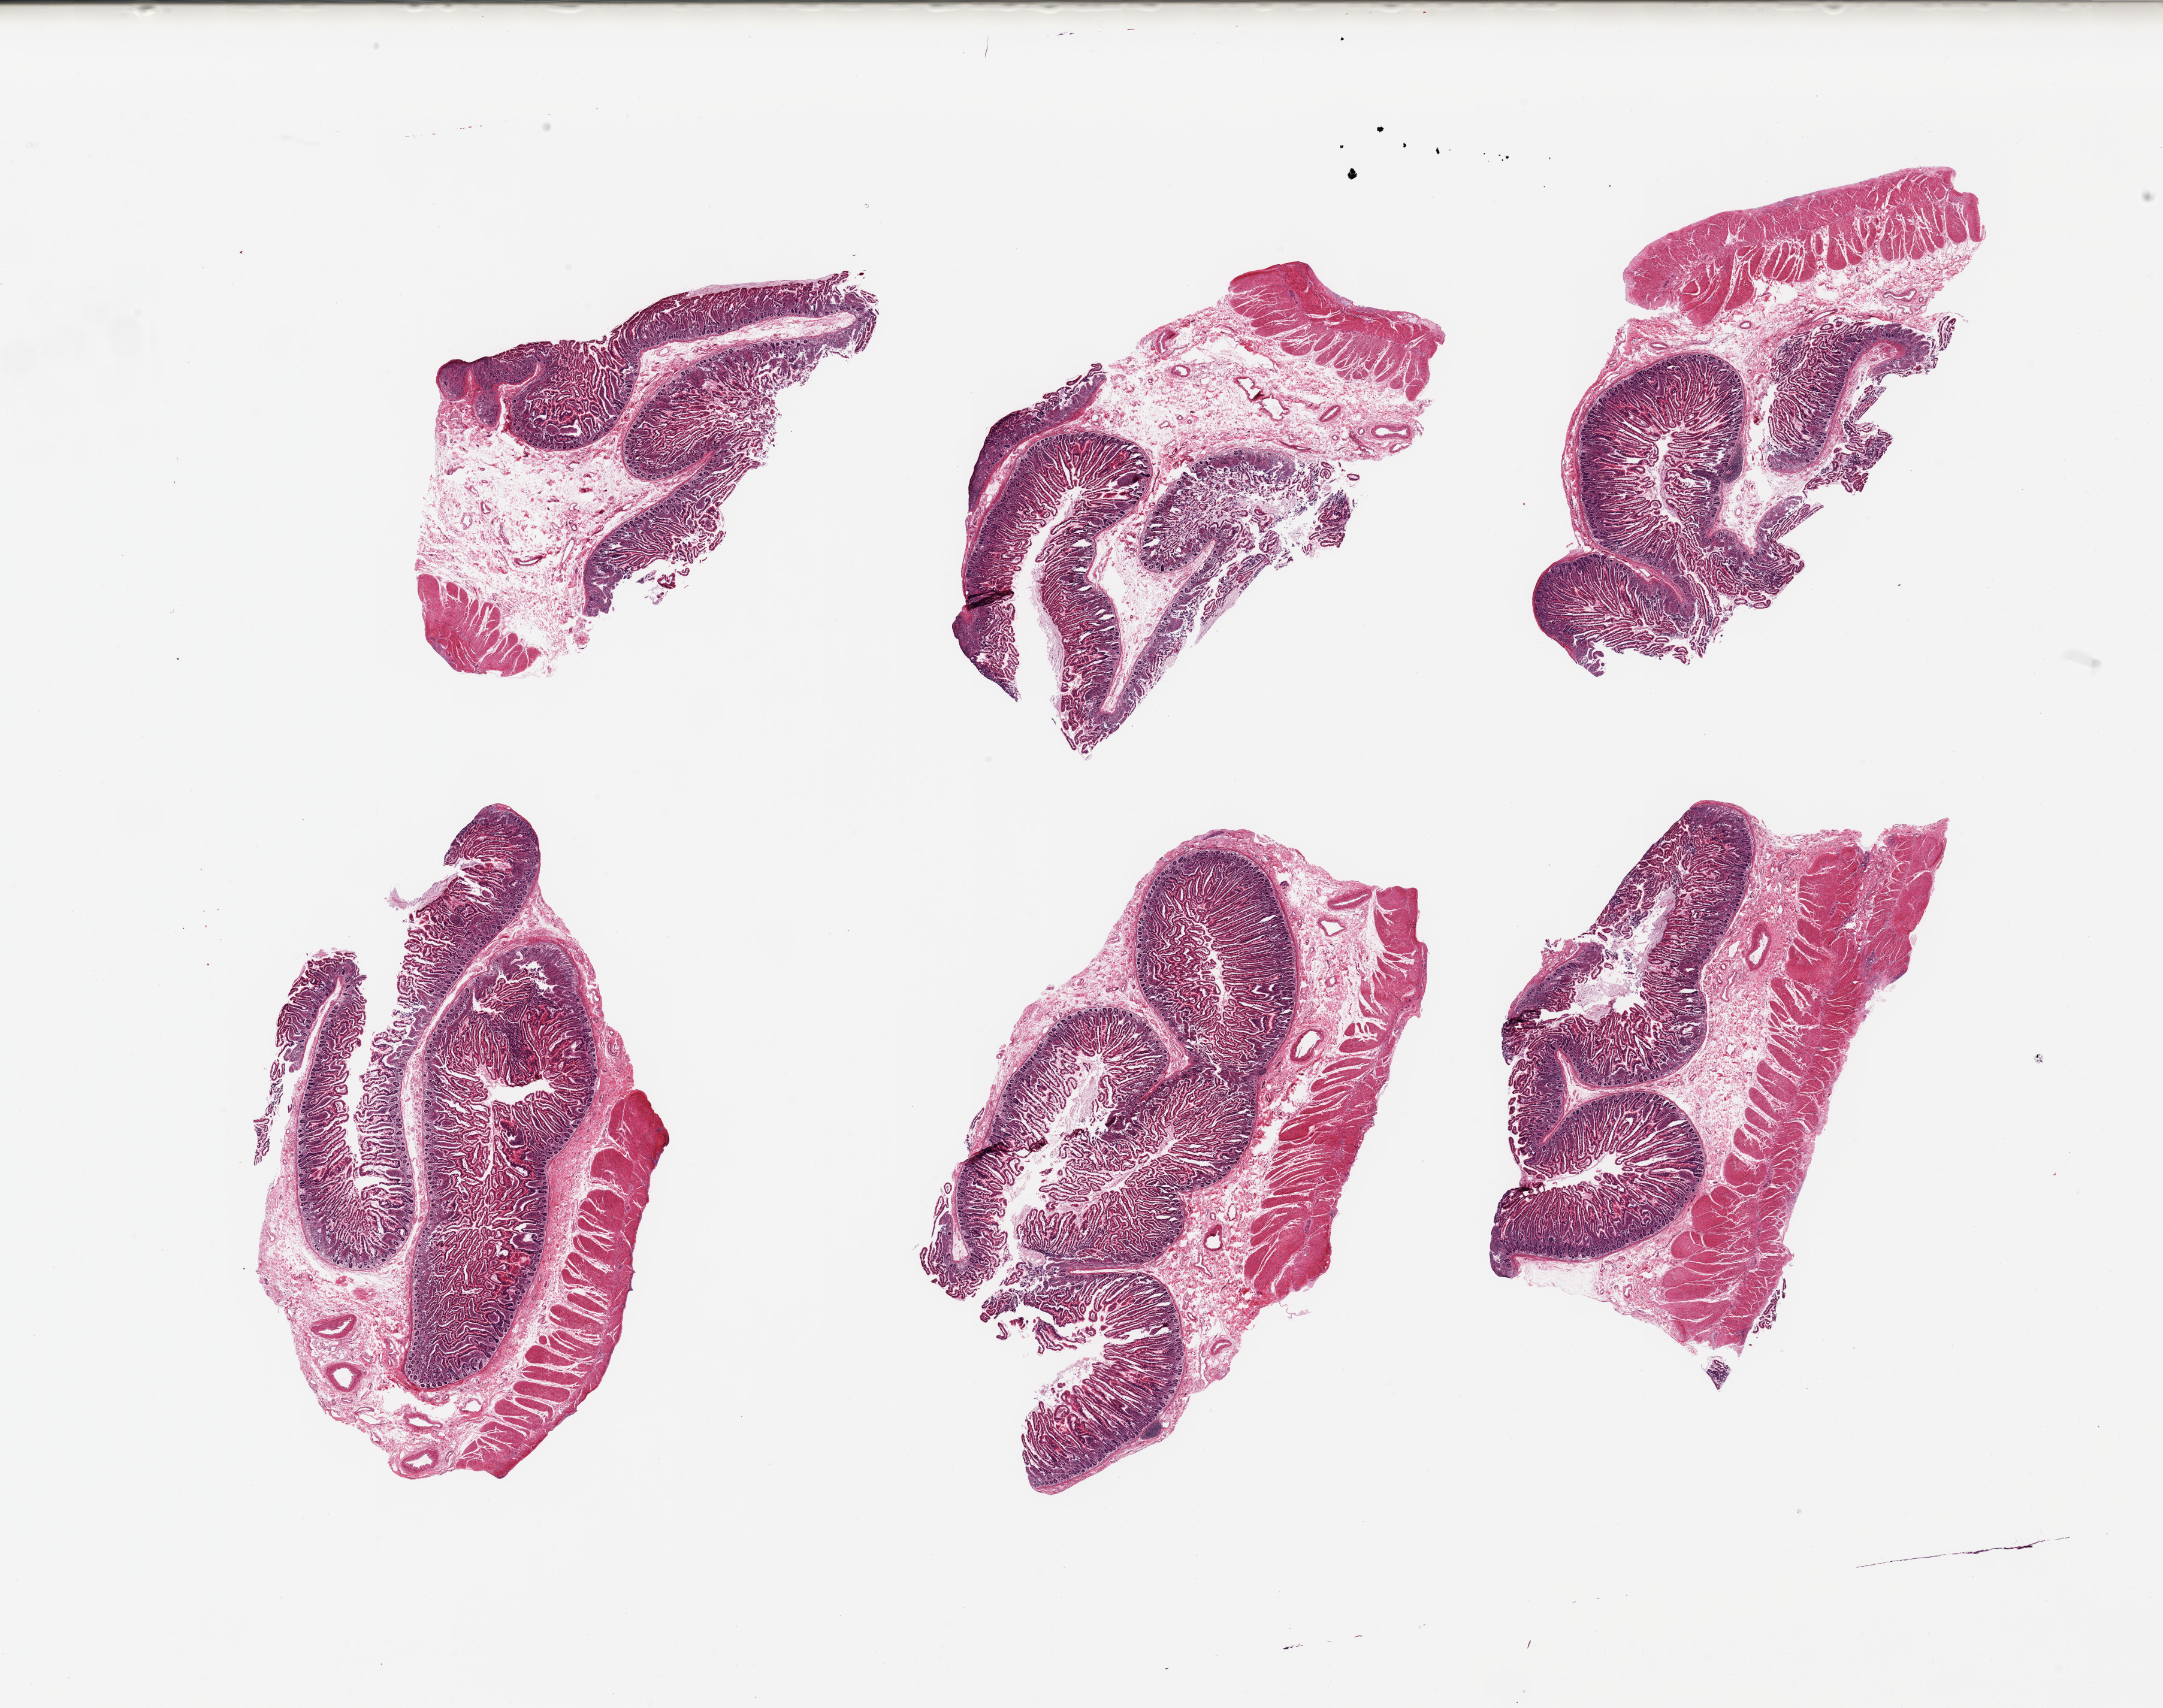
Hematoxylin and eosin (H&E) whole-slide image, brightfield, a low-resolution overview of the entire scanned area, about 28.5 x 22.5 mm (acquisition: 20x scan). PAXgene-fixed paraffin-embedded (PFPE) section. Target tissue: transverse colon. Donor tissue sample. Donor sex: male.
Pathologist's review note for this sample: 6 pieces, small bowel, no lymphoid aggregates, not c/w terminal ileum.